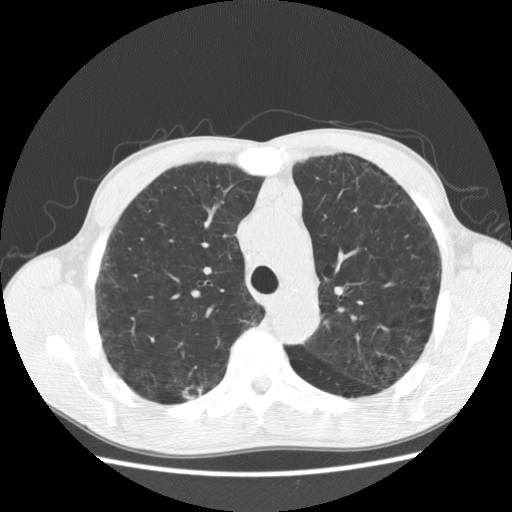
Low-dose screening chest CT, one axial slice; slice 137 of 195 in the series (ordered by position); lung window (W 1500 / L -600 HU); 2.5 mm slice thickness; 512 × 512 image matrix.
Outlined on this slice (manually delineated by an expert):
- lesion 1 (tumor, upper lobe of right lung): bounding box <183,387,193,399> (left, top, right, bottom; pixels)